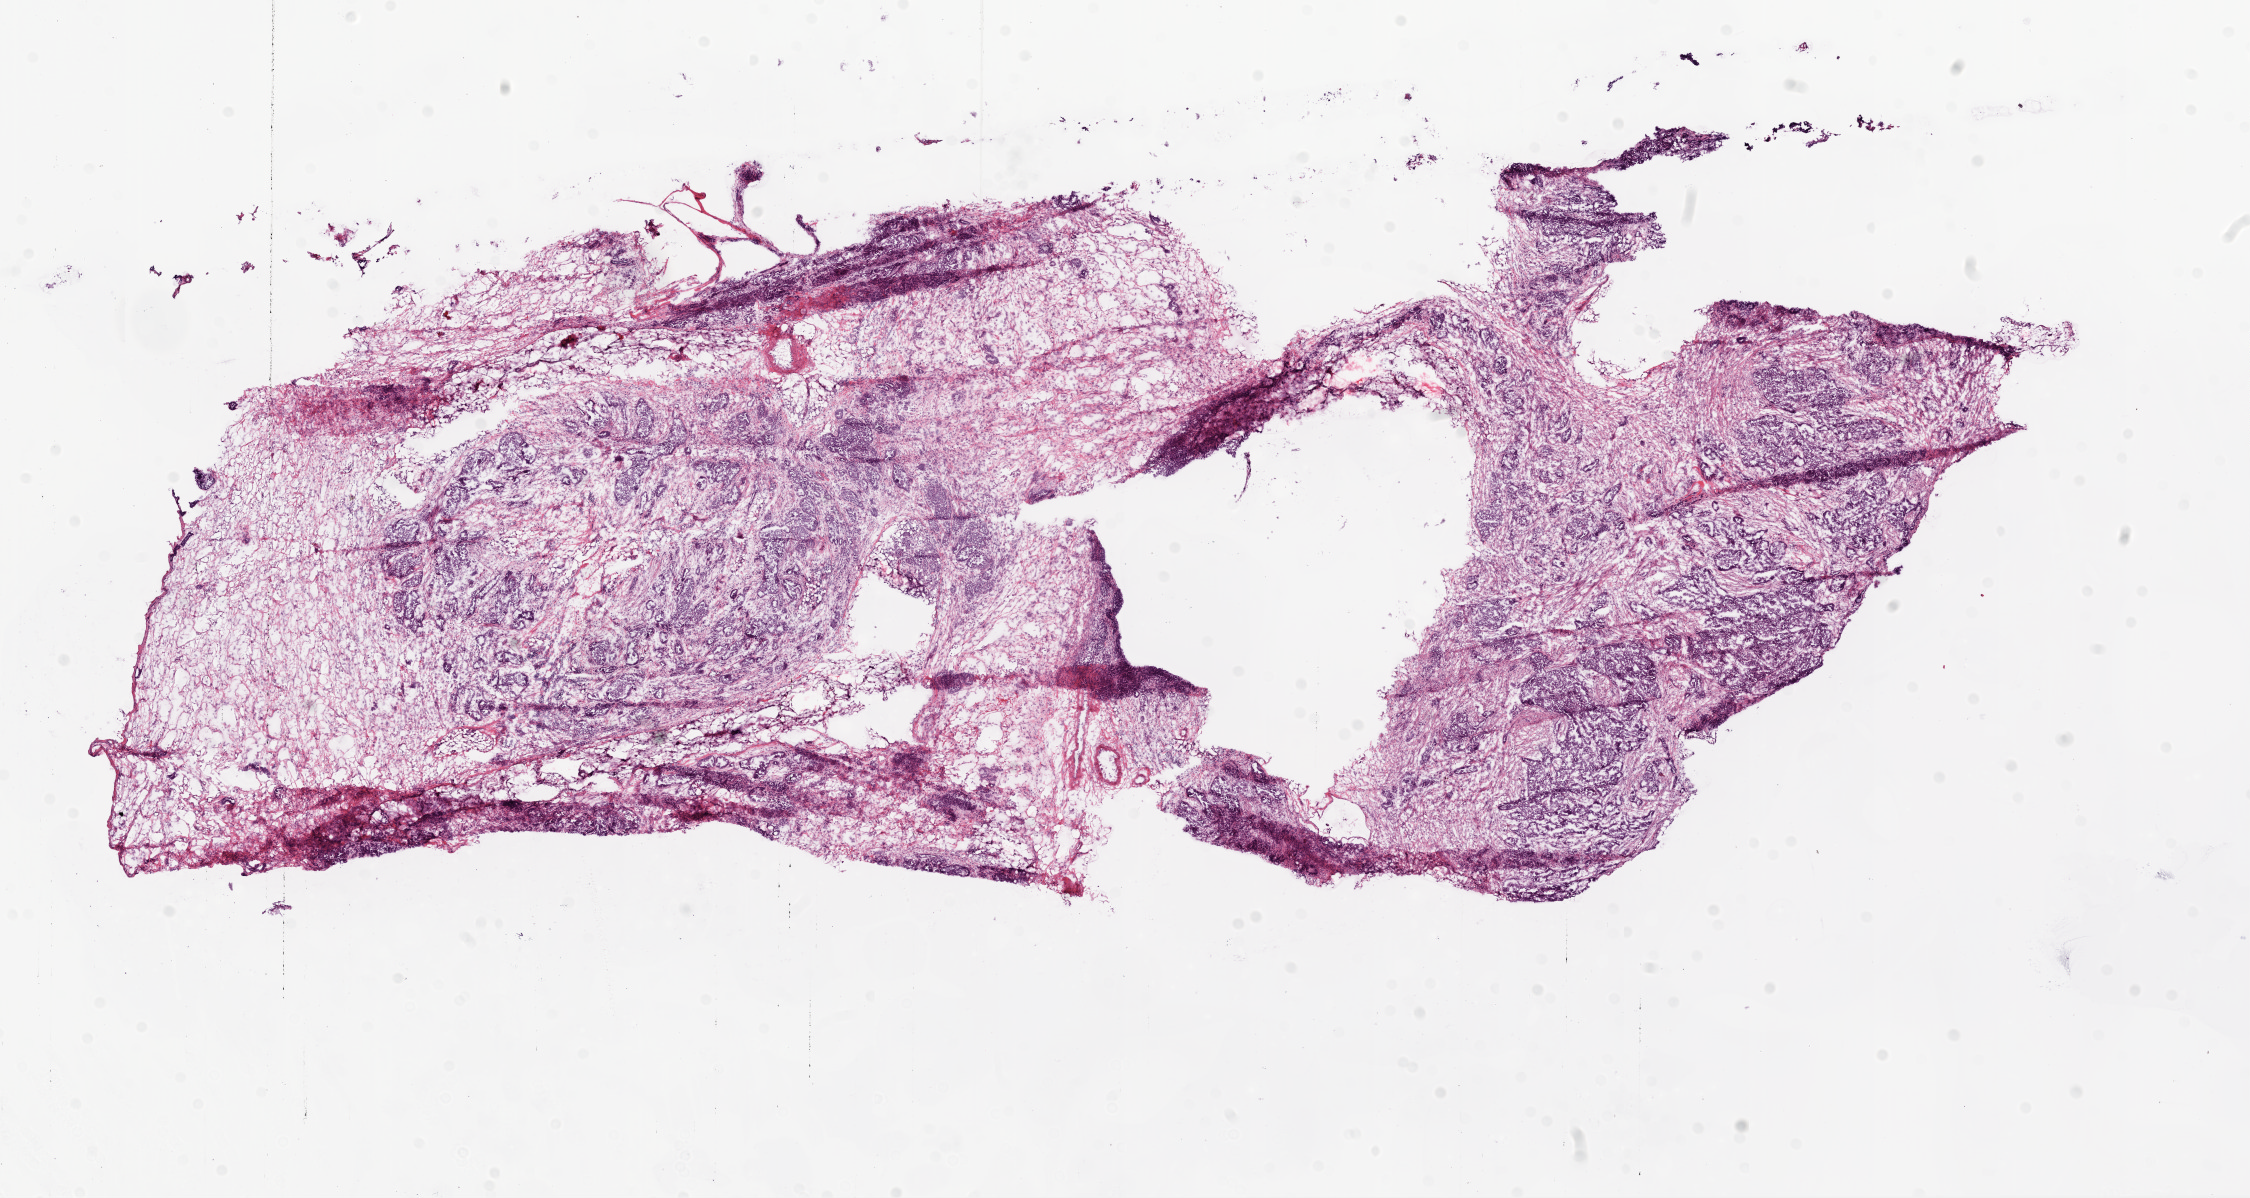
Whole-slide histology image, Hematoxylin and eosin (H&E) stained — a low-resolution overview of the entire scanned area, about 18.1 x 9.6 mm, frozen section from the bottom of the tissue portion, sample: primary tumour, ovary. Patient: female, age at initial diagnosis 47 years. Histologic grade: G3 (poorly differentiated). Slide review estimates, as recorded: tumour cells 40%, tumour nuclei 66%, normal cells 58%, stromal cells 0%, necrosis 2%.
Diagnosis: Serous cystadenocarcinoma, NOS.